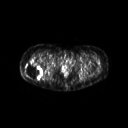
FDG PET of an extremity soft-tissue mass (from a PET/CT study), one axial slice. Slice 40 of 267 in the series (ordered by position). 3.27 mm slice thickness. 128 × 128 image matrix, field of view 600 × 600 mm. Female patient, age 57 years. From the clinical record (not read from this slice): histological type: epithelioid sarcoma with vascular differentiation; site of the primary tumour: right buttock.
Structures marked on this image (expert contour drawn on MRI and transferred to this co-registered scan by the dataset authors):
- gross tumour volume (mass): bounding box [x1, y1, x2, y2] px = [24, 60, 44, 80]